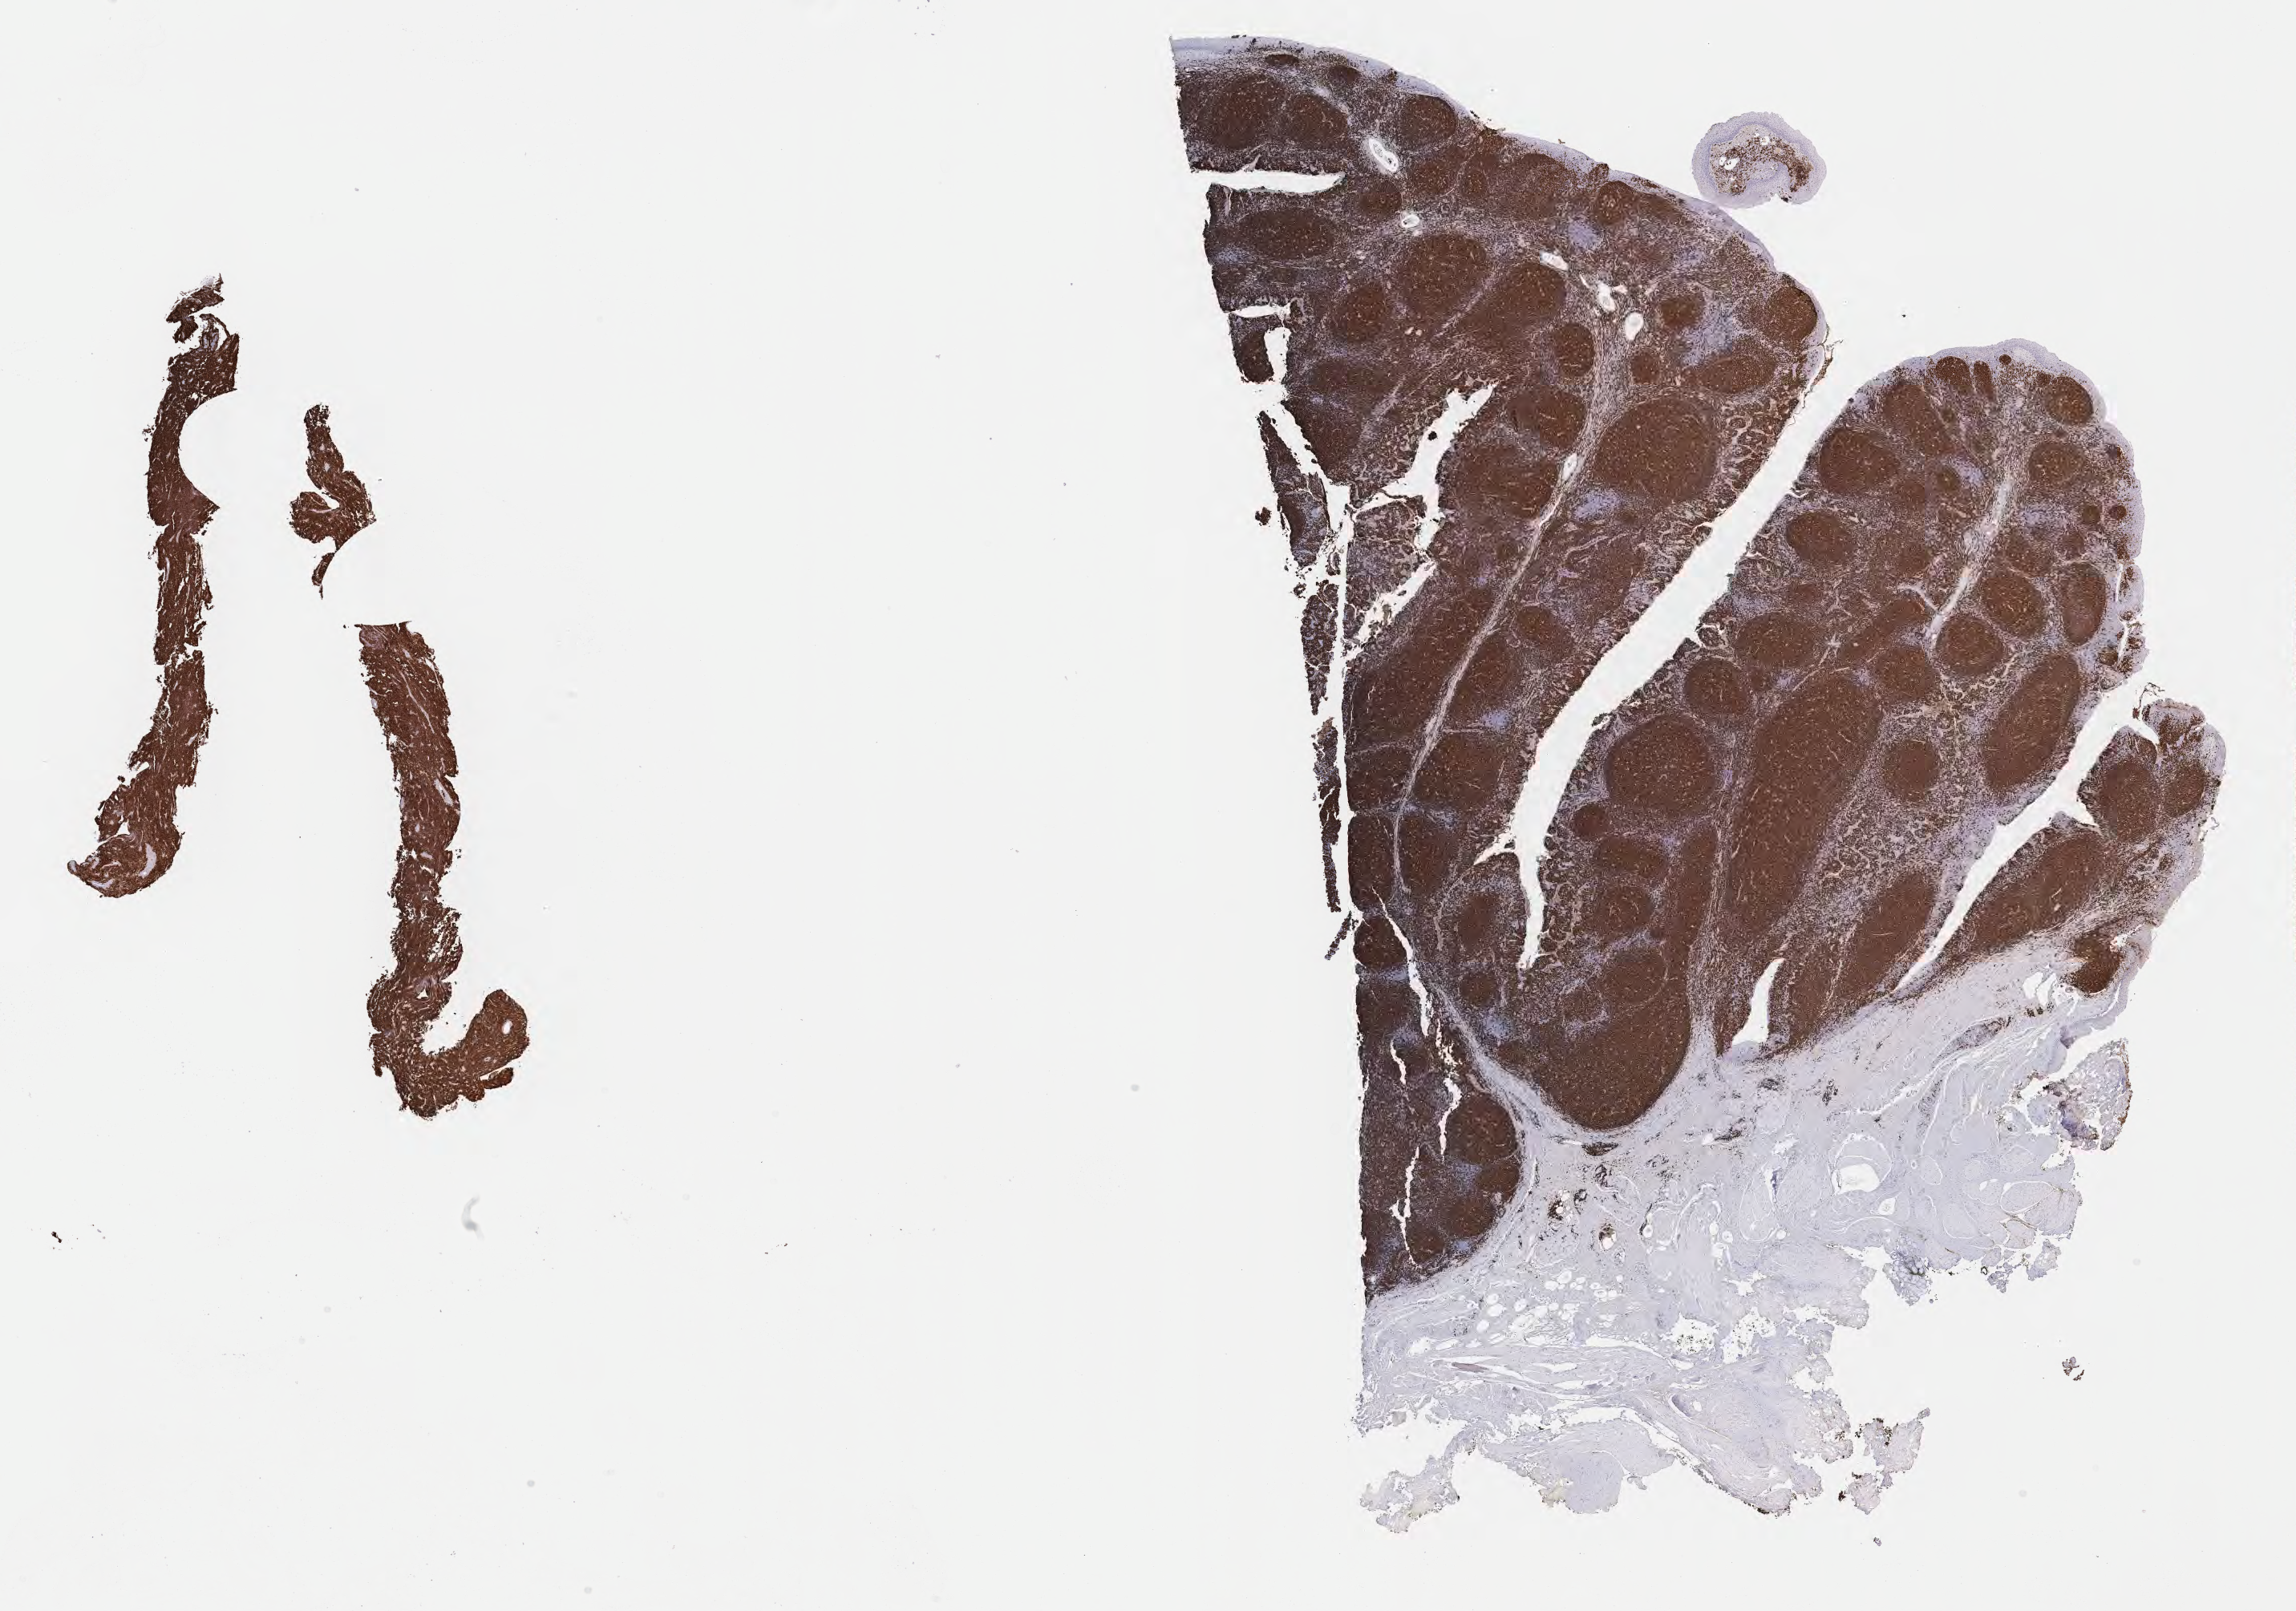
Whole-slide image, immunohistochemical stain for CD20 — whole scanned area (about 23.2 x 16.2 mm) shown as a low-resolution overview, specimen: tumor tissue, anatomic site: spleen. Male patient; age at initial diagnosis 6 years.
Diagnosis: Burkitt lymphoma, NOS.